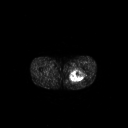
FDG PET of an extremity soft-tissue mass (from a PET/CT study), one axial slice; position 255 of 267 along the scan axis; 3.27 mm slice thickness; 128 × 128 image matrix, field of view 700 × 700 mm. Patient: male, 44 years. Case-level facts recorded for this patient, not image findings: histological type: undifferentiated pleomorphic liposarcoma; grade: high; site of the primary tumour: left thigh.
Annotated regions visible in this slice (expert contour drawn on MRI and transferred to this co-registered scan by the dataset authors):
- gross tumour volume including surrounding oedema: bounding box <68,70,84,82> (left, top, right, bottom; pixels)
- gross tumour volume (mass): <69,70,83,81>